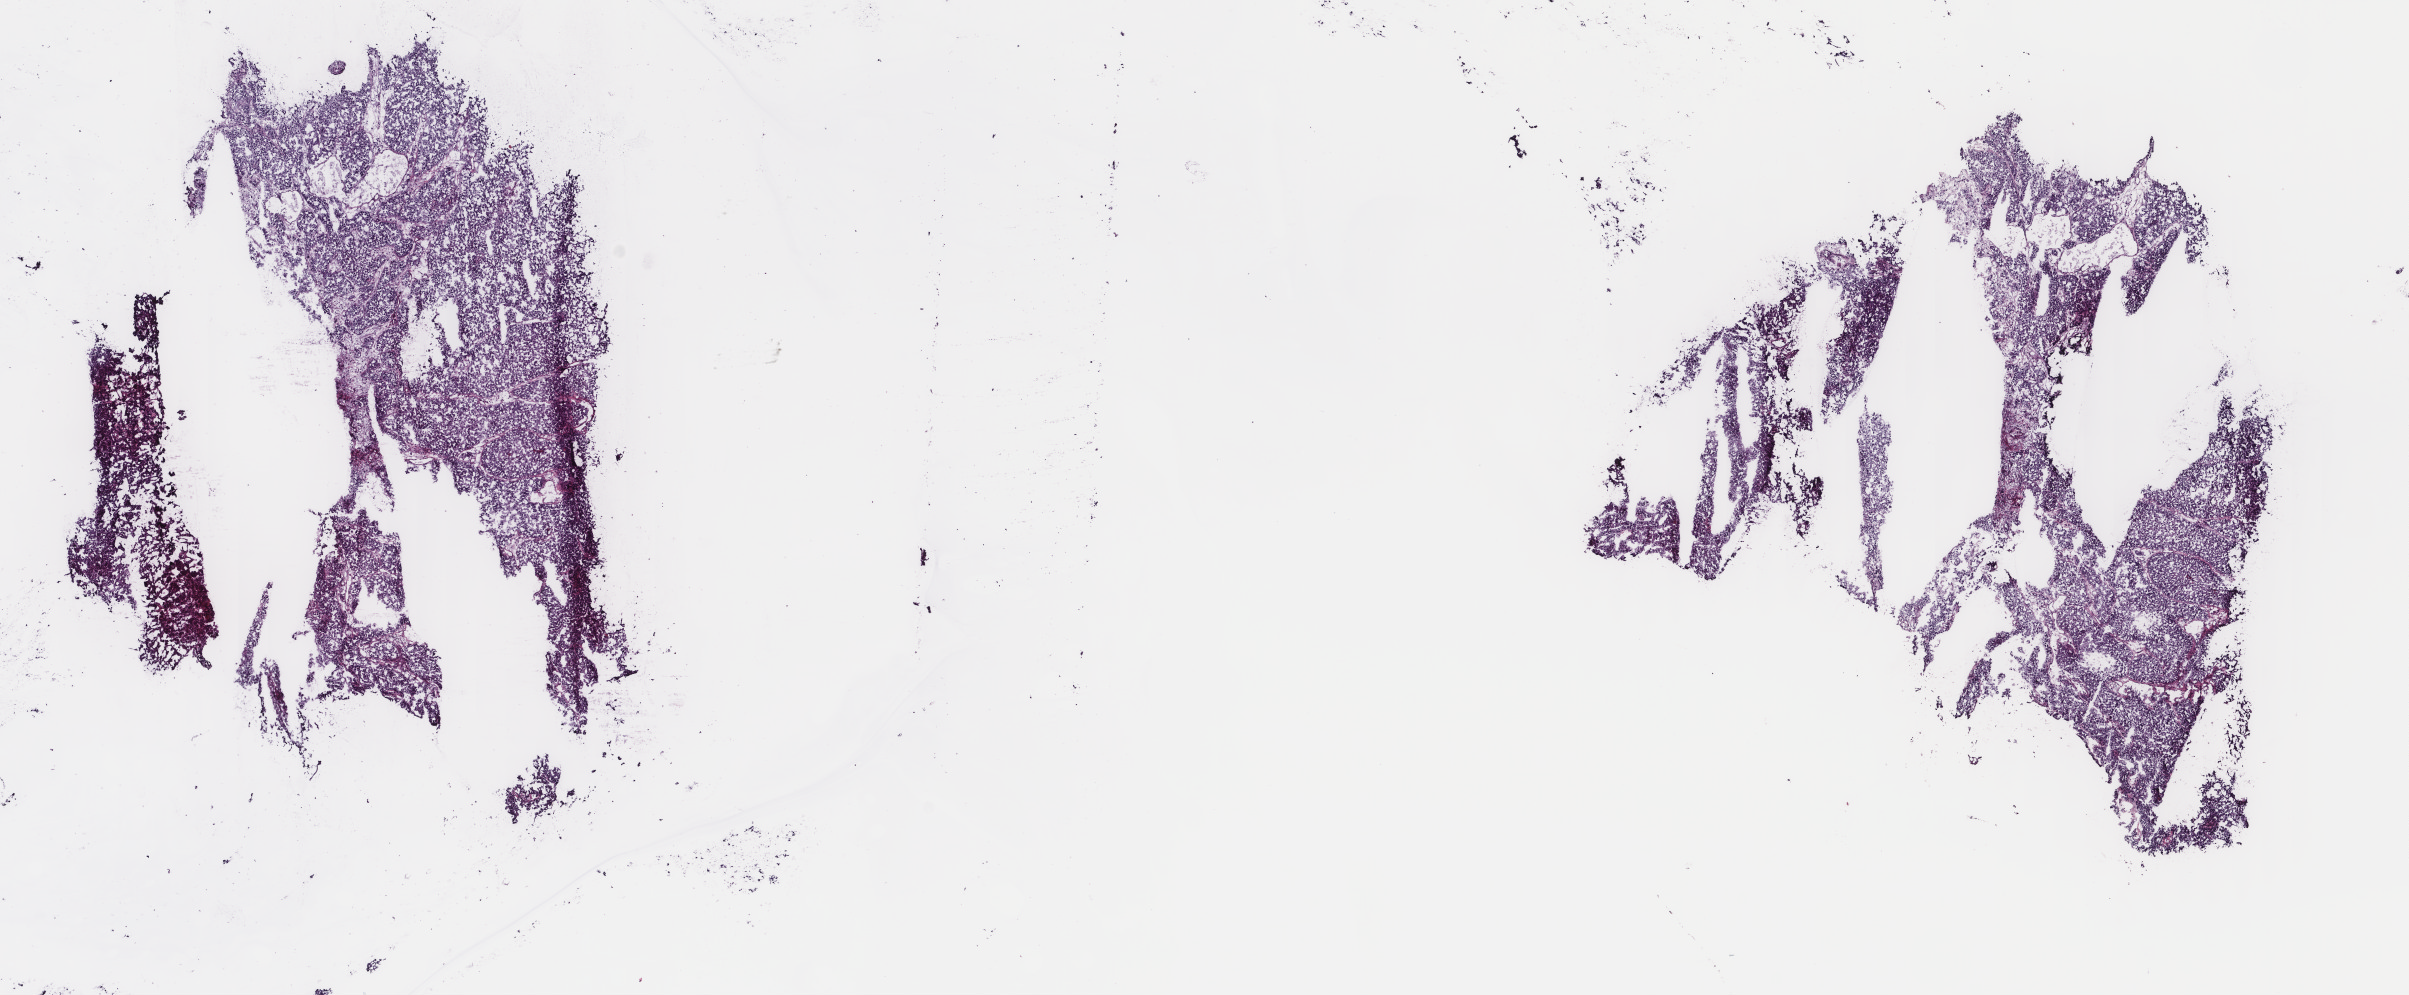
H&E-stained whole-slide image, whole scanned area (about 19.1 x 7.9 mm) shown as a low-resolution overview. Frozen section. Primary tumour sample from the bladder. Male patient; age at initial diagnosis 66 years. Histologic grade: high grade. Slide review estimates, as recorded: tumour cells 100%, tumour nuclei 90%, normal cells 0%, stromal cells 0%, necrosis 0%. Inflammatory infiltration, as recorded: lymphocyte infiltration 0%, monocyte infiltration 0%, neutrophil infiltration 0%.
AJCC pathologic stage: II (7th edition). Histologic diagnosis: Transitional cell carcinoma.